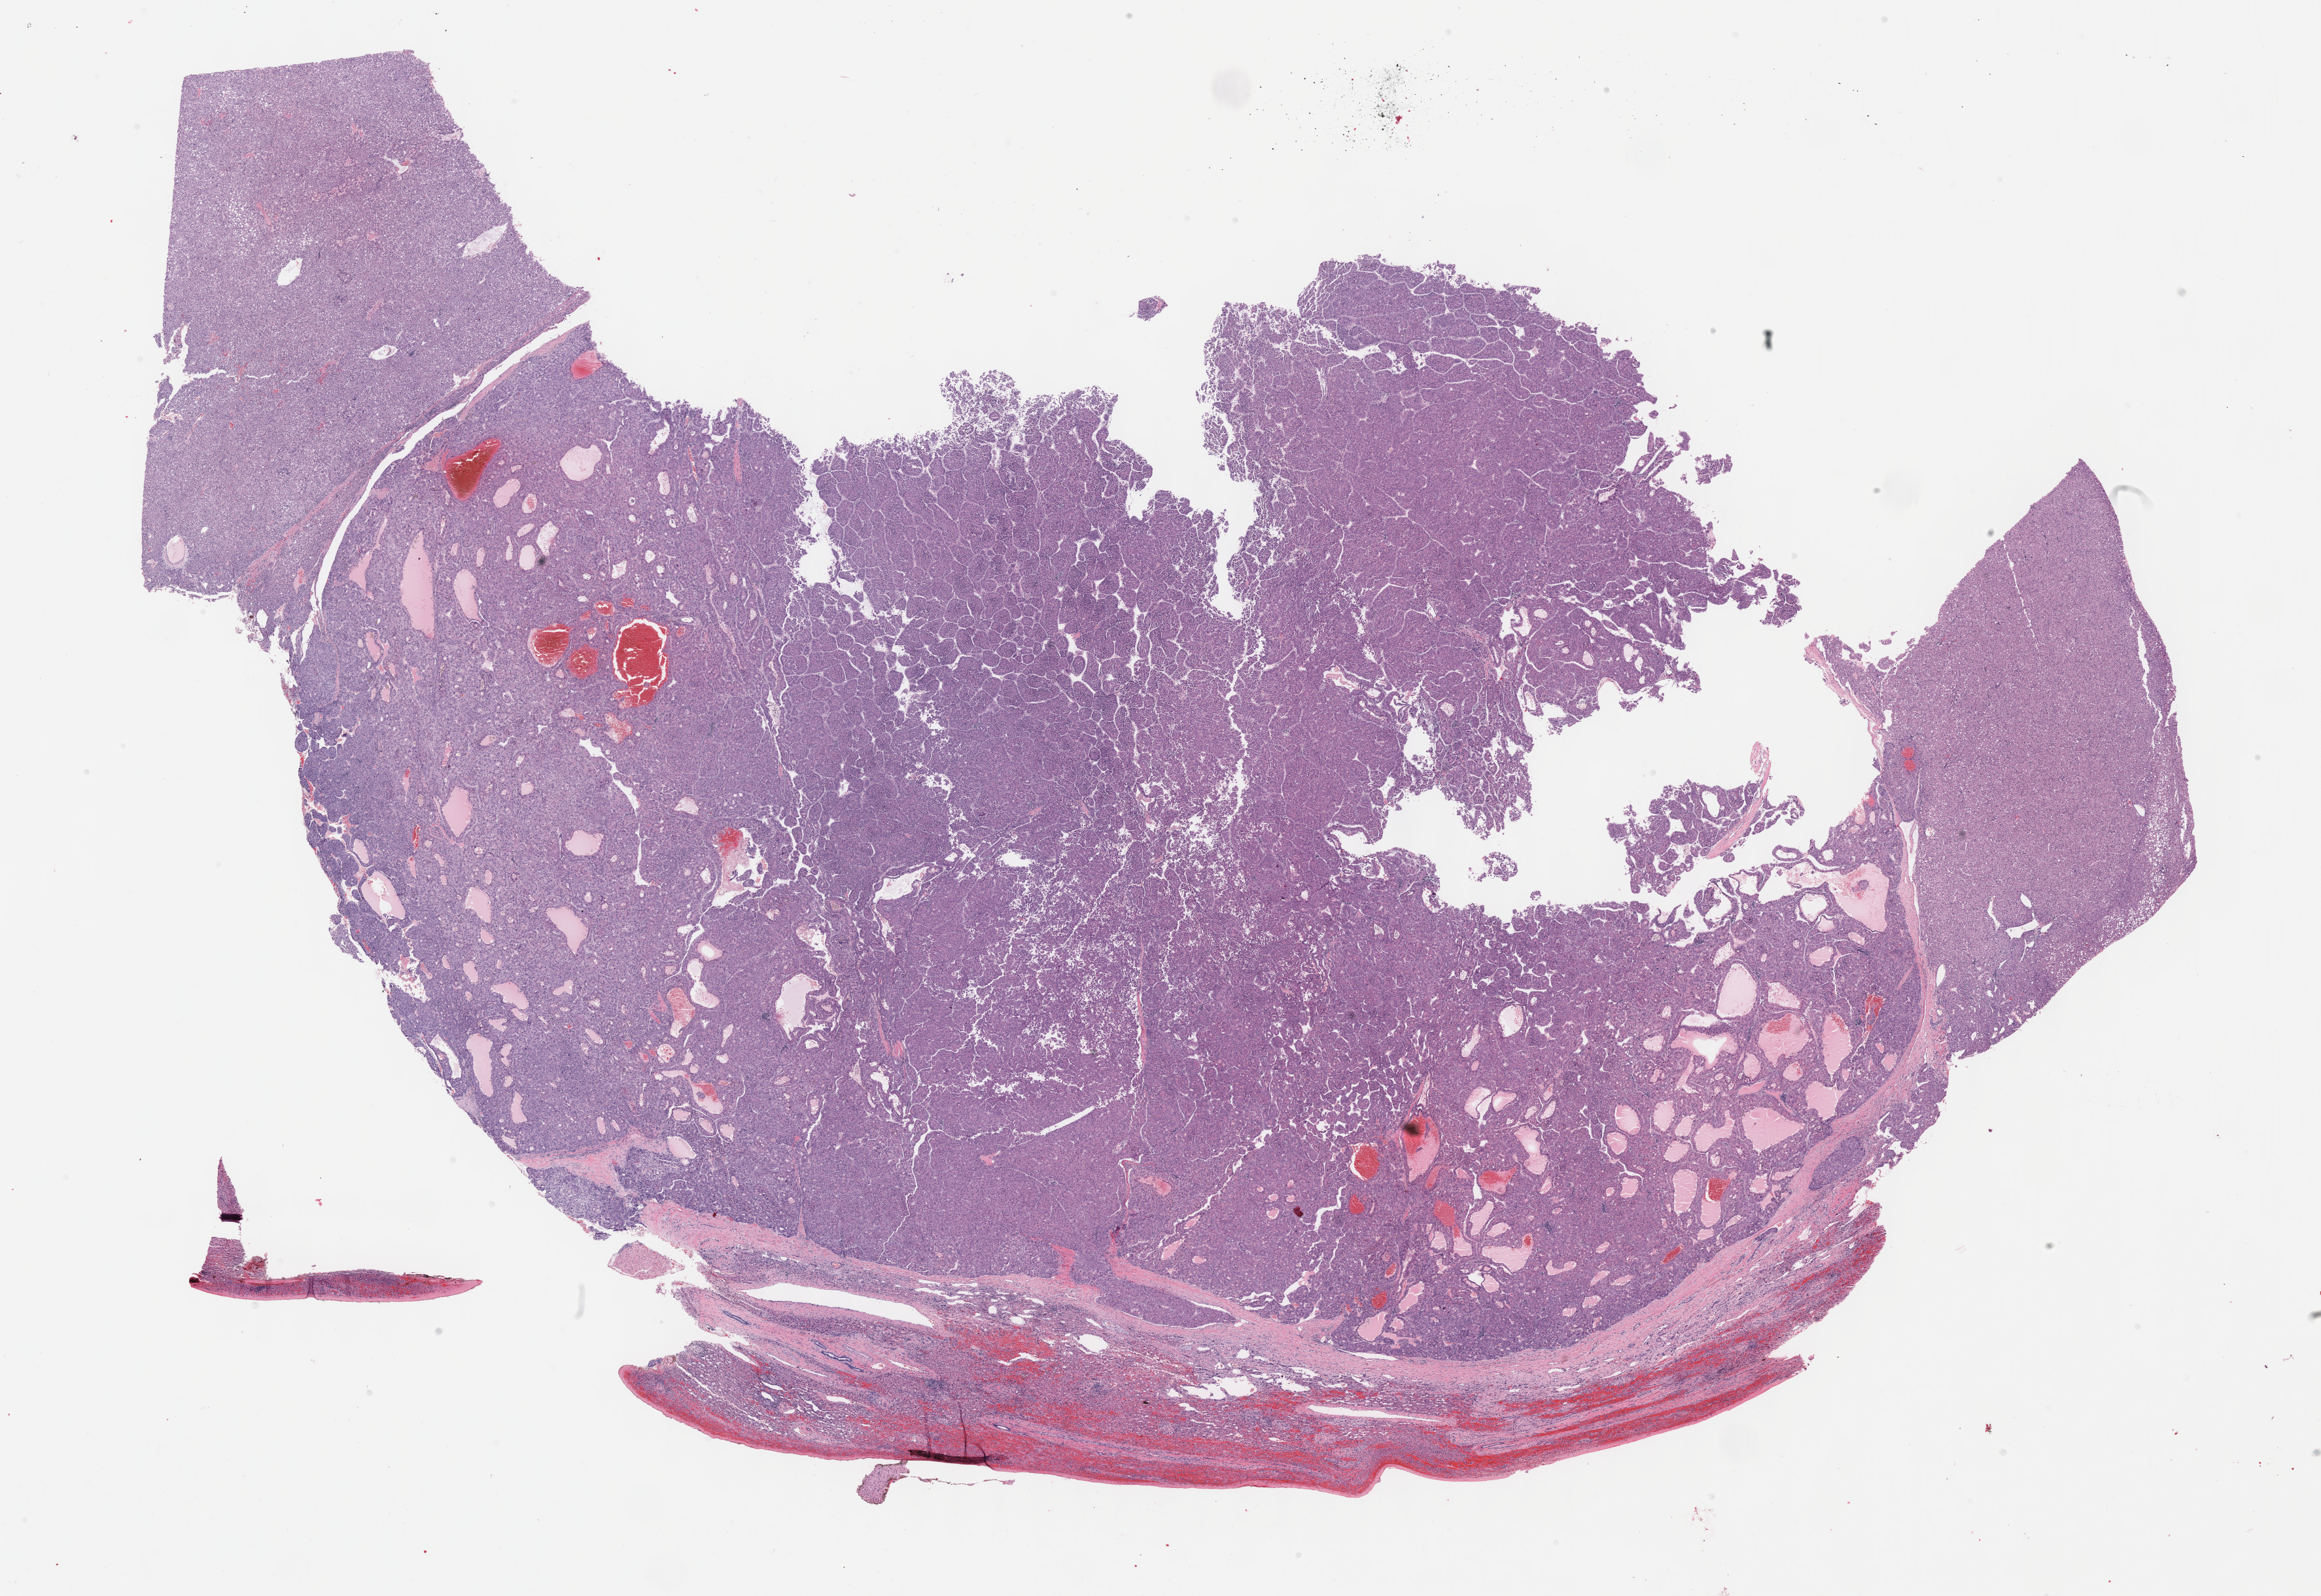
Hematoxylin and eosin (H&E) stained whole-slide image — shown as a low-resolution overview of the whole scanned area (about 28.7 x 19.7 mm, acquisition: 40x scan), formalin-fixed paraffin-embedded (FFPE) diagnostic section, liver, primary tumour sample. Patient: male, age at initial diagnosis 68 years. Histologic grade: G2 (moderately differentiated).
- AJCC pathologic stage: IIIA (7th edition)
- diagnosis: Hepatocellular carcinoma, NOS